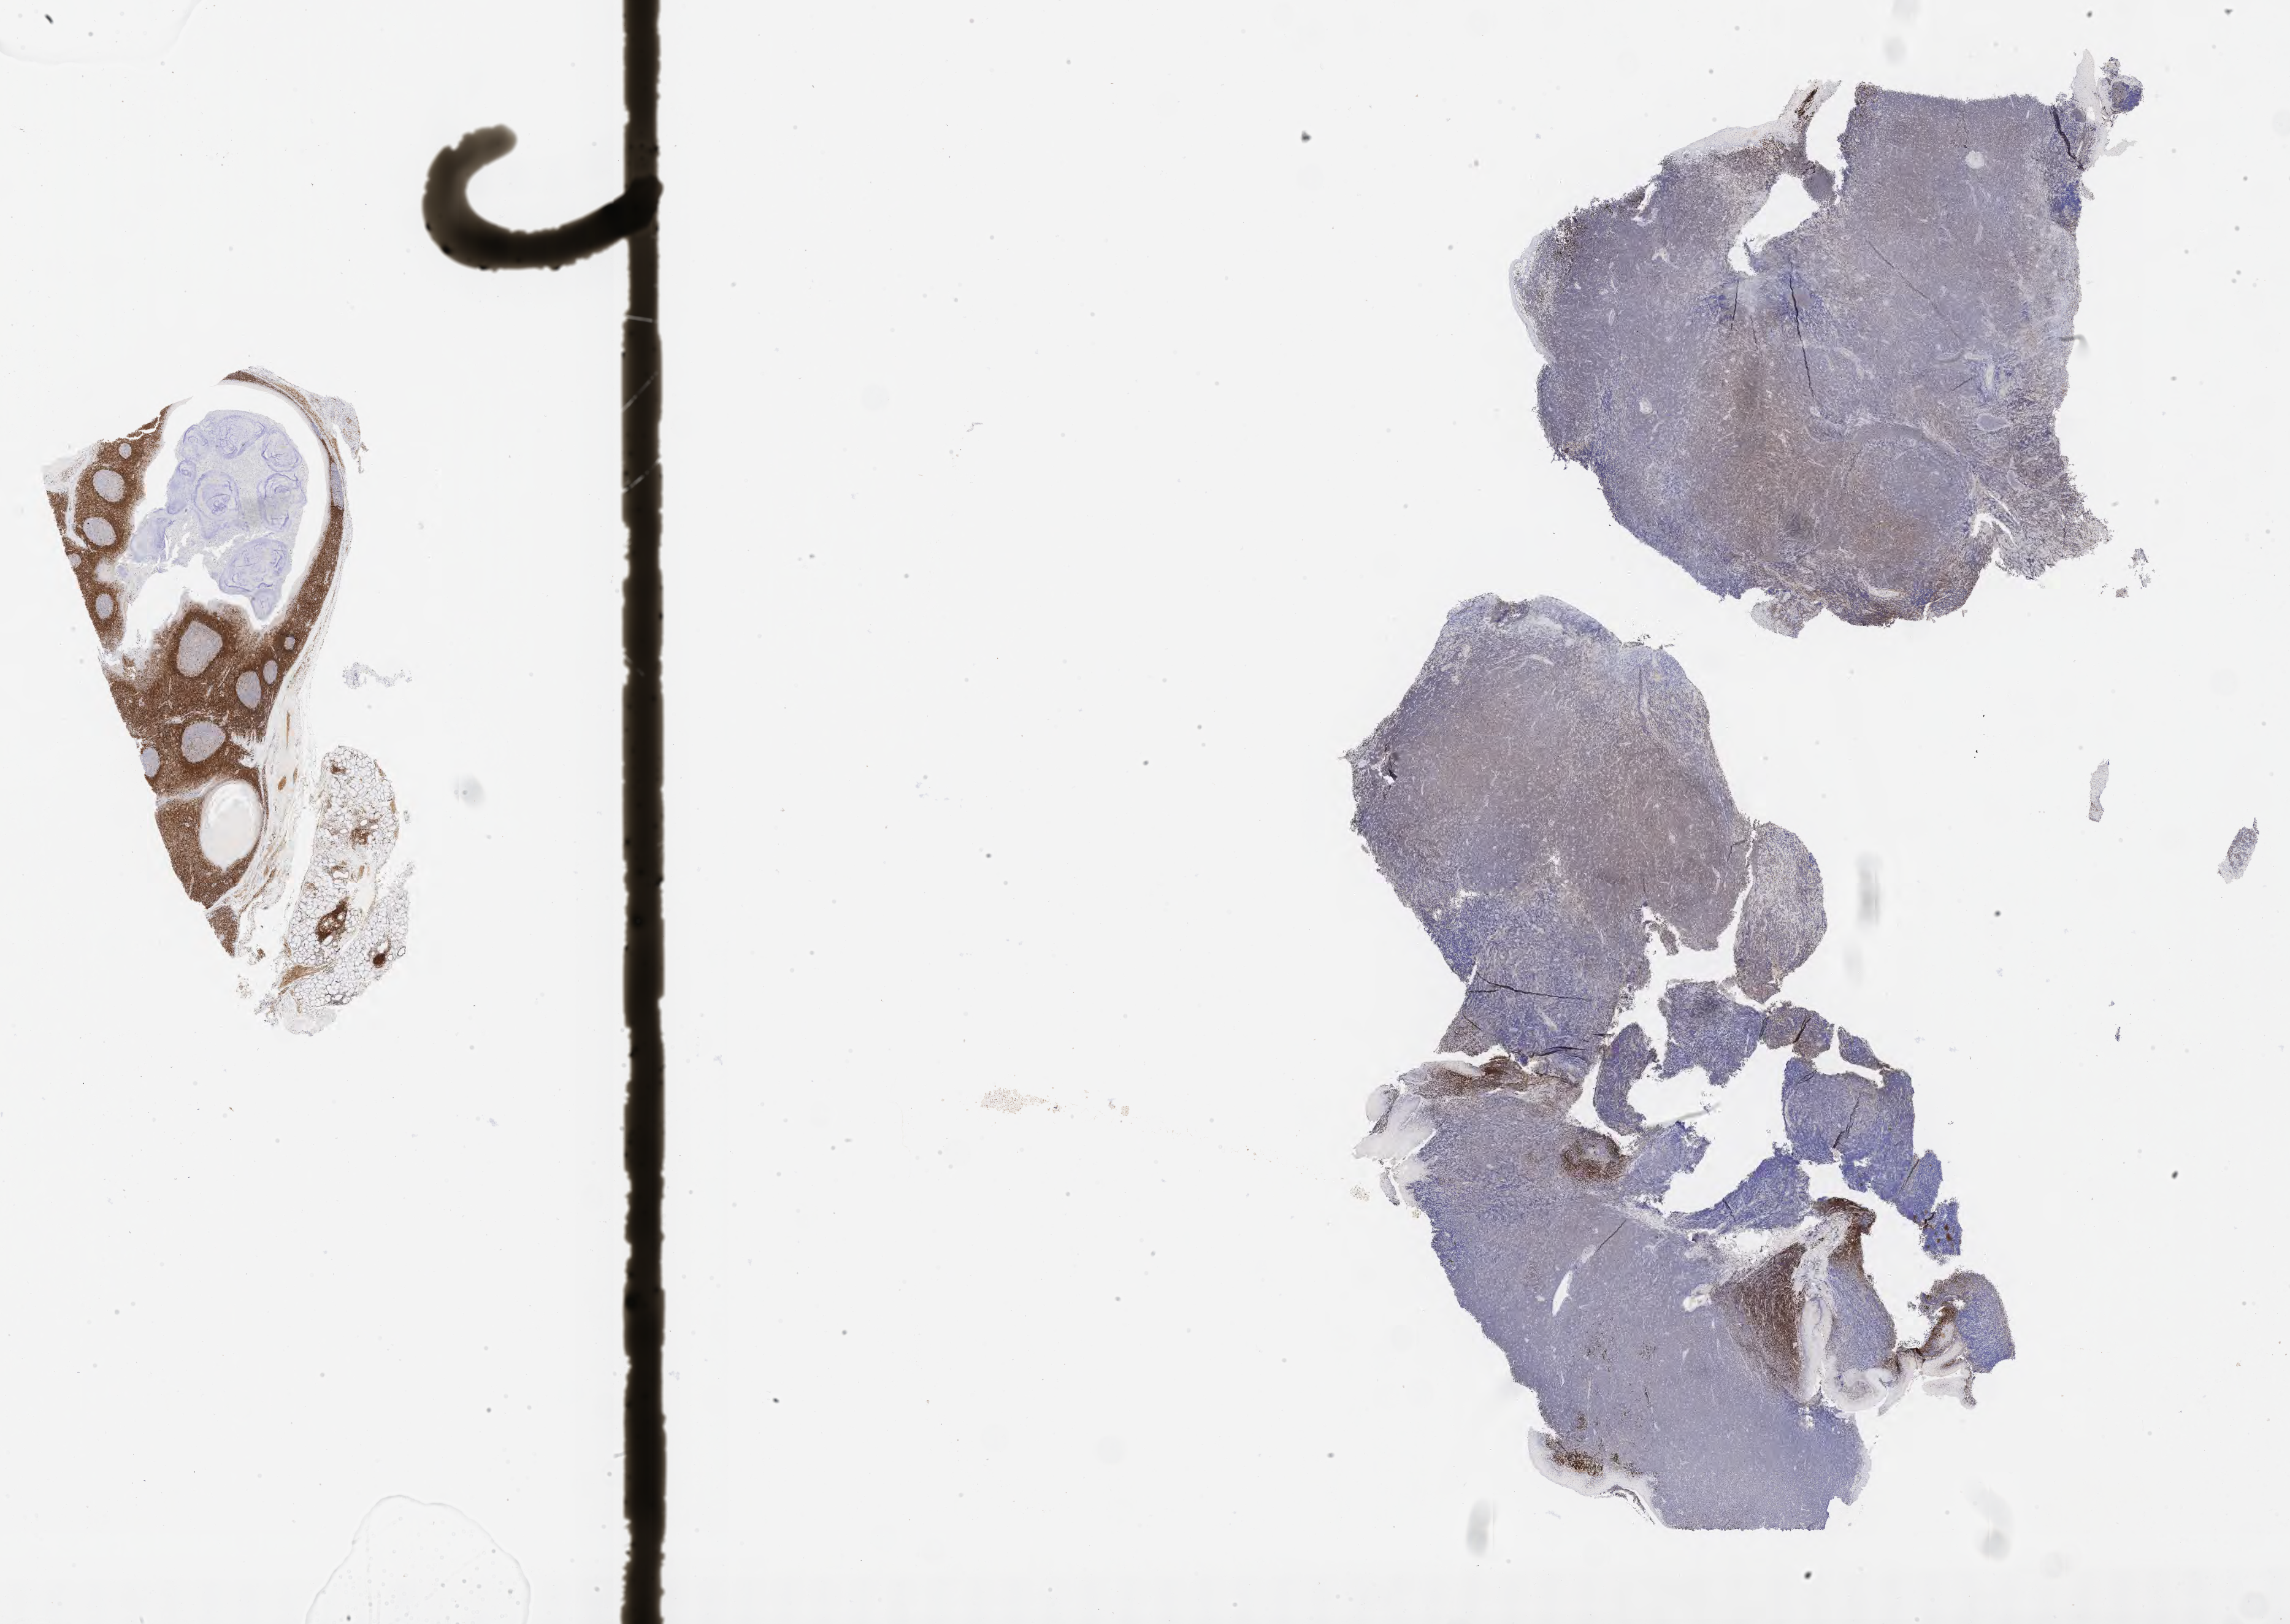
Immunohistochemistry (IHC) whole-slide image stained for BCL2, shown as a low-resolution overview of the whole scanned area (about 30.2 x 21.4 mm), tumor tissue. Patient male; age 22 years.
Histologic diagnosis: Diffuse large B-cell lymphoma, NOS.